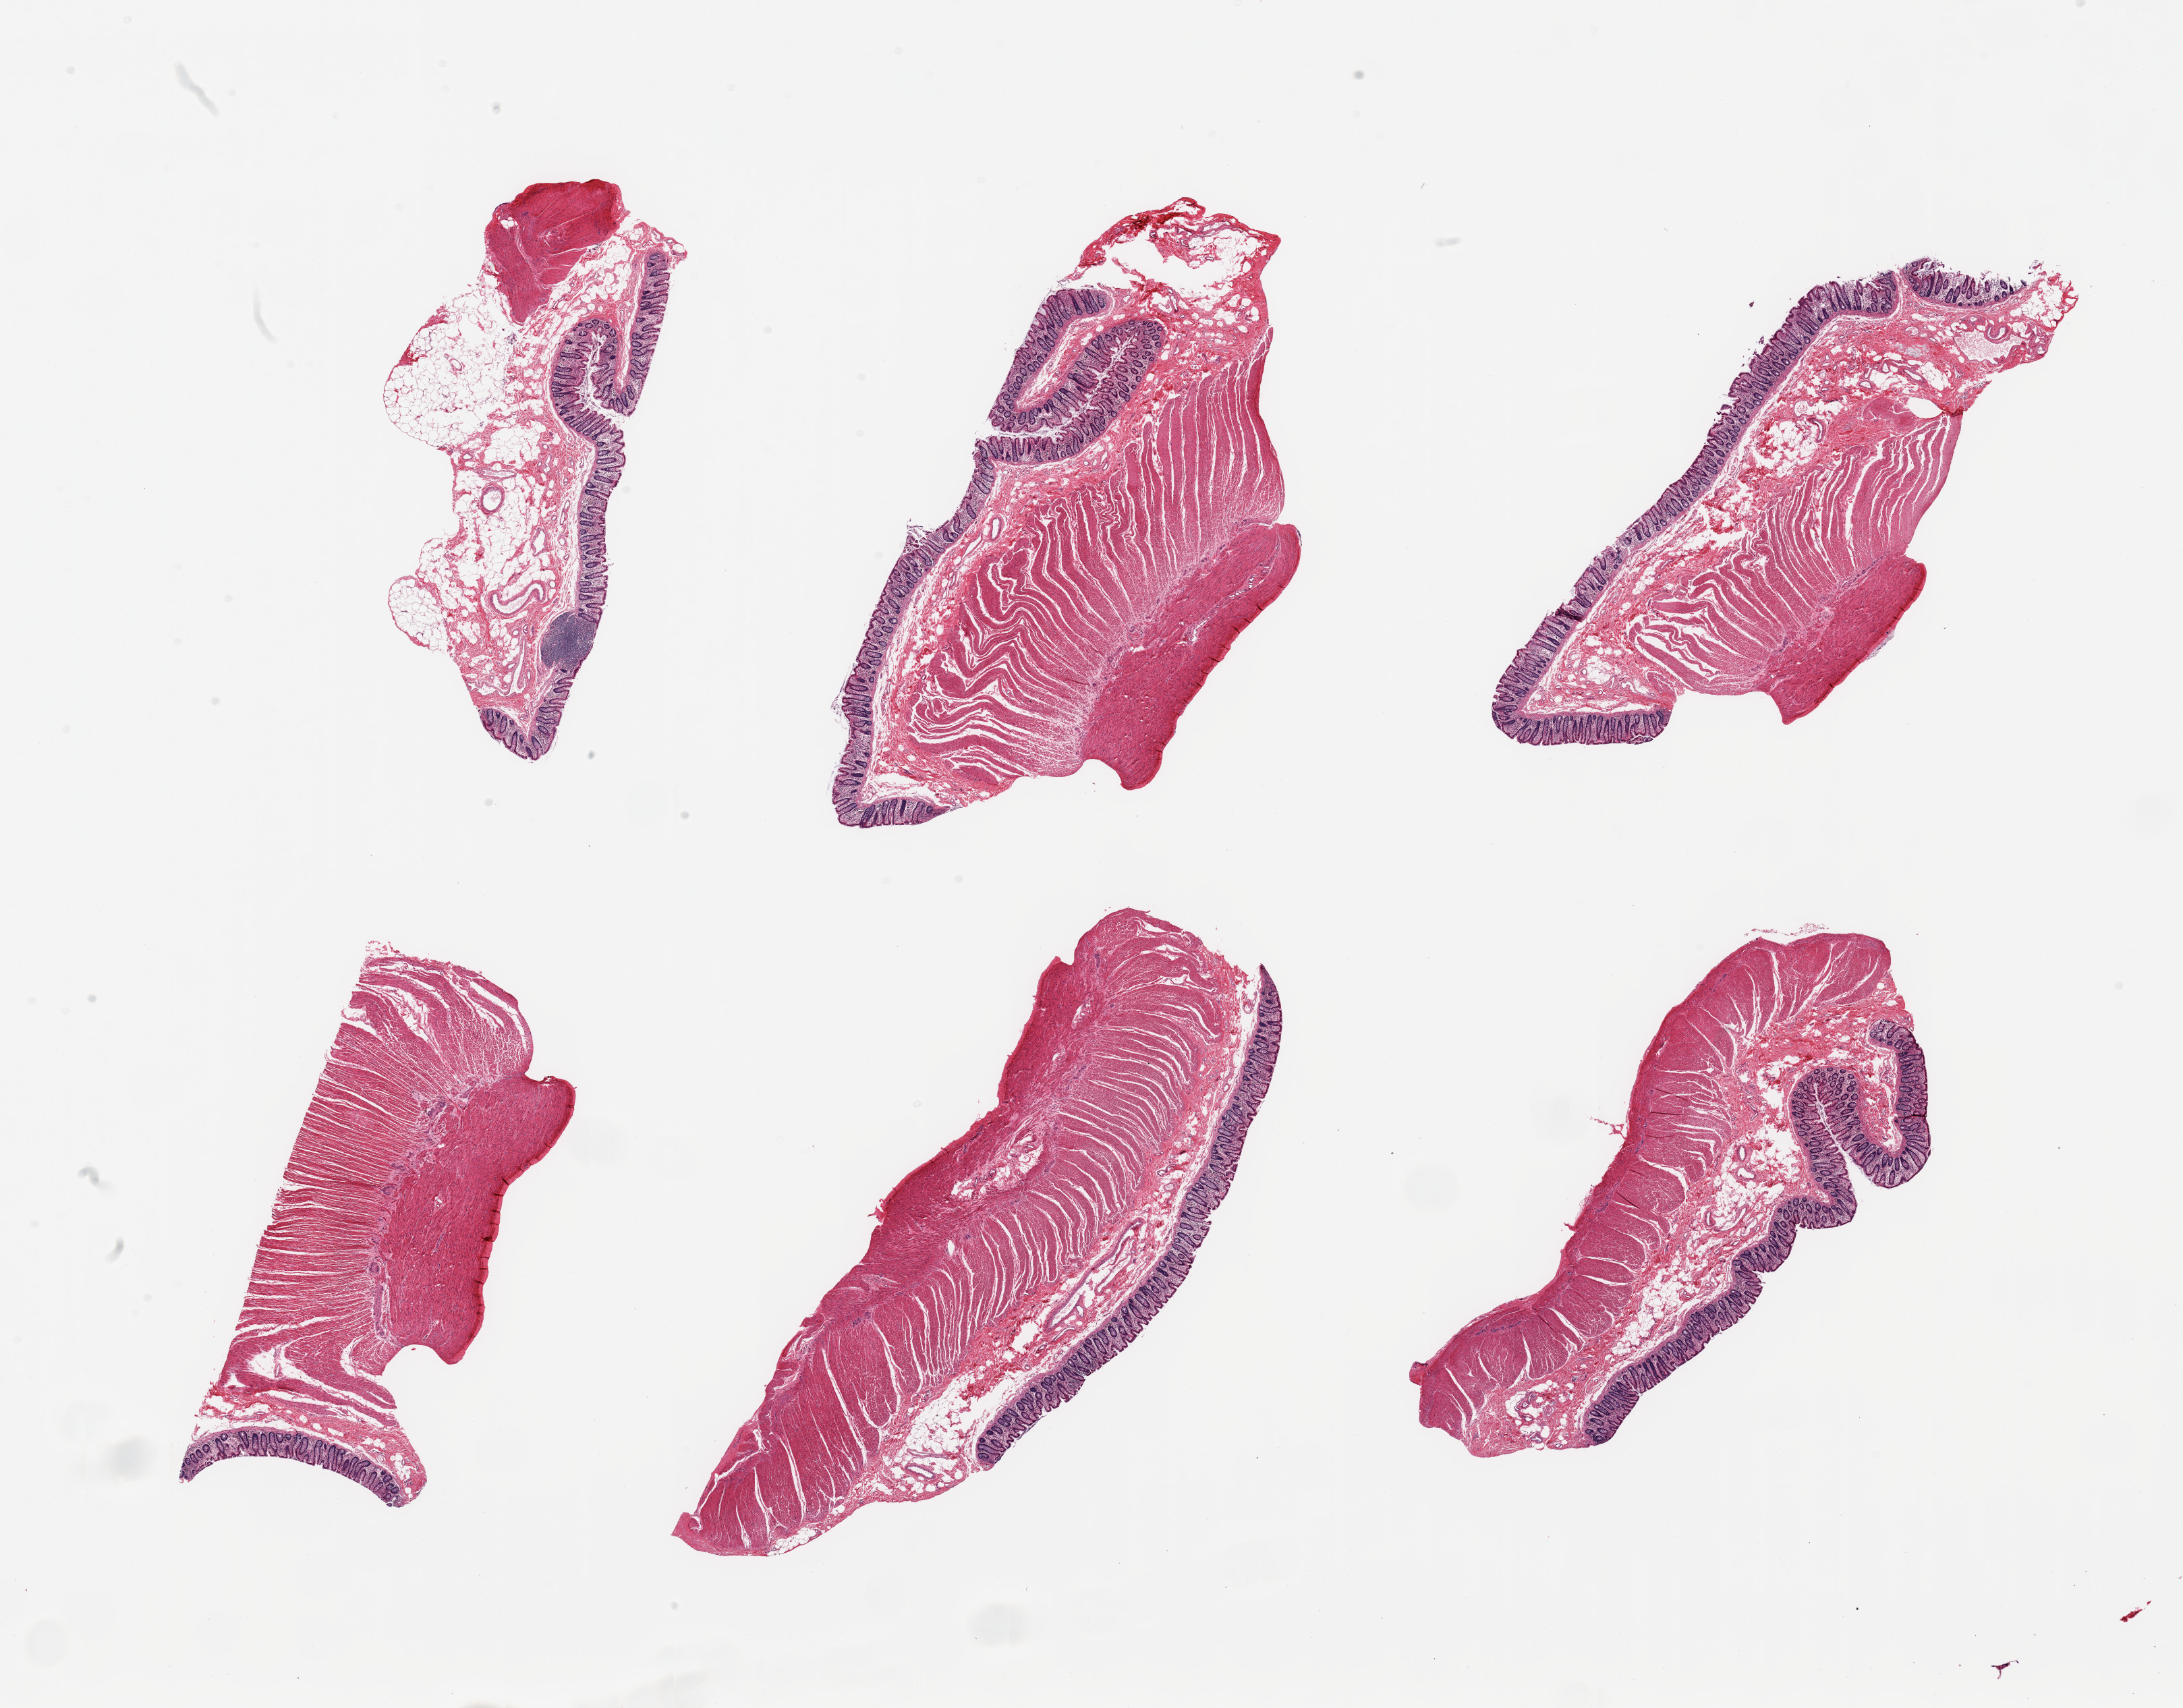
H&E whole-slide image, brightfield, shown as a low-resolution overview of the whole scanned area (about 25.6 x 20.0 mm). PAXgene-fixed, paraffin-embedded tissue. Section of transverse colon (target tissue). Tissue donor sample. Donor sex: male.
• reviewer comment on this tissue sample: 6 pieces; mucosa and muscularis, one piece includes ~50% fat, melanosis coli